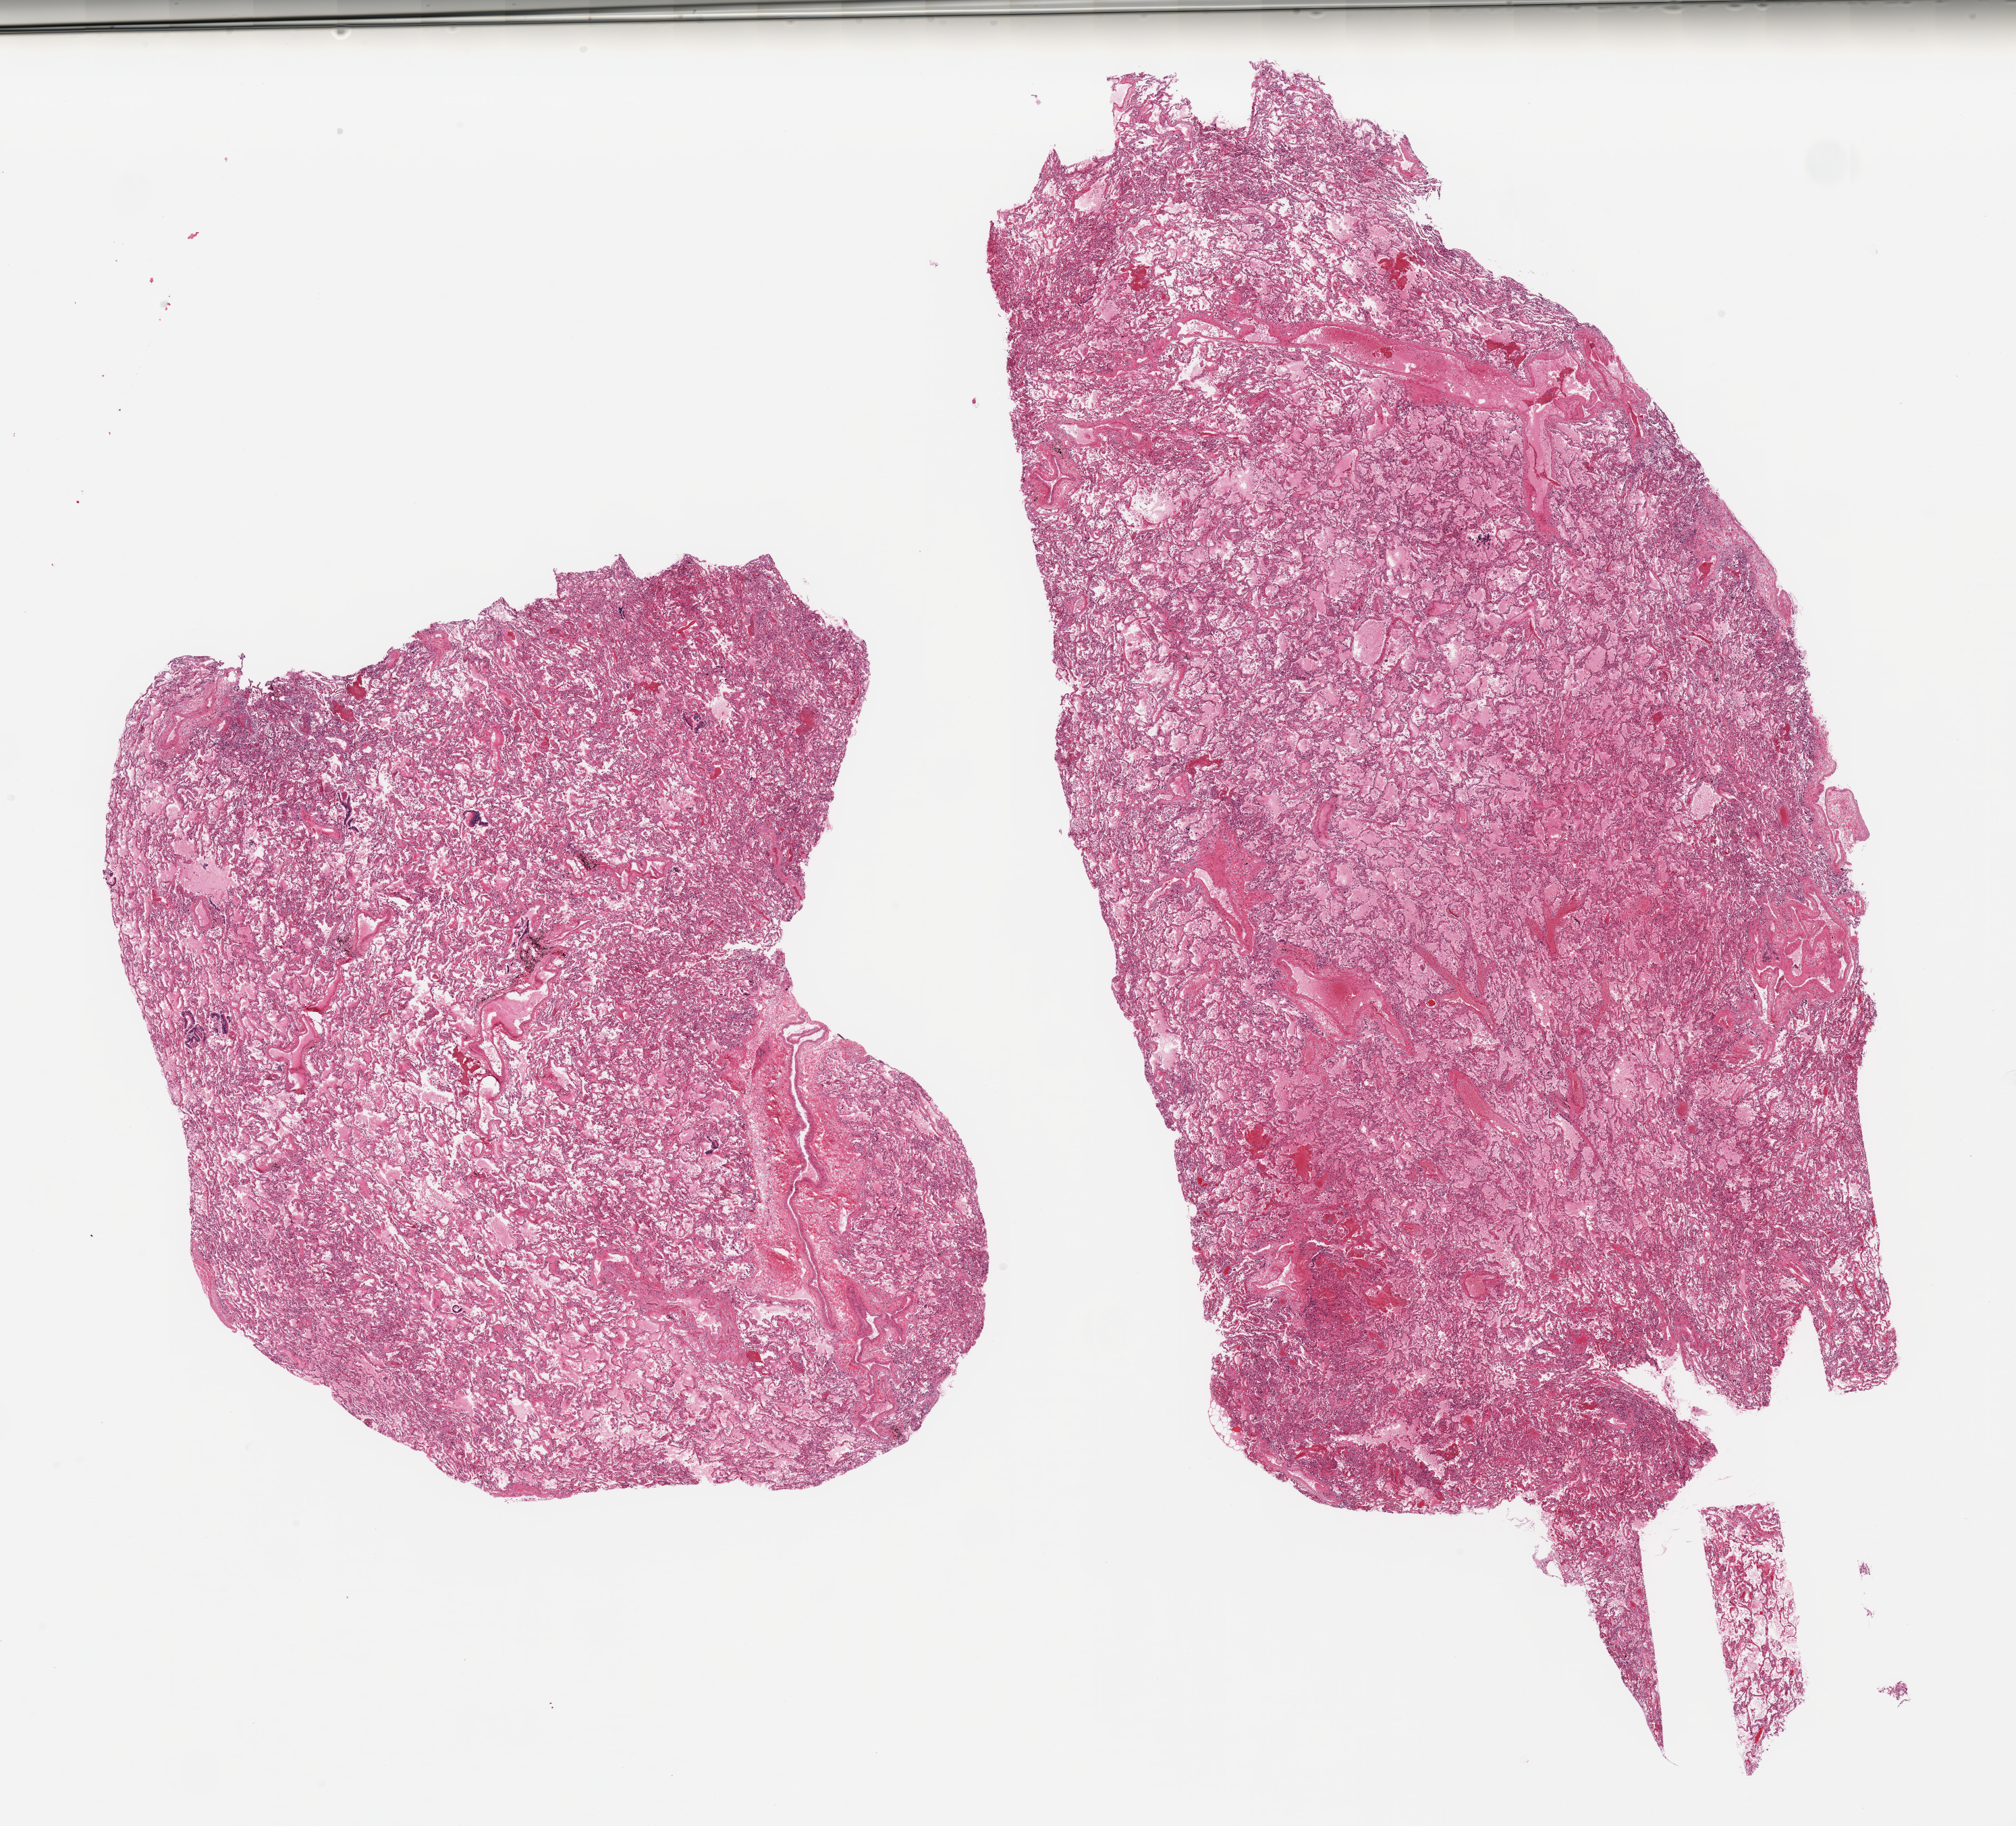
Digitized haematoxylin and eosin-stained section, brightfield — low-resolution overview of the scanned area, about 23.6 x 21.4 mm, PAXgene-fixed paraffin-embedded (PFPE) section, target tissue: lung, tissue donor sample. Male donor.
• reviewer comment on this tissue sample: 2 pieces; pulmonary edema & early pneumonia; no sign of chronic disease